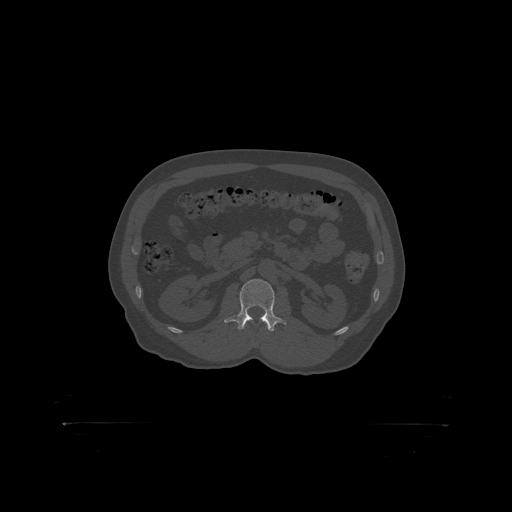
CT including the spine, one axial slice. Slice 302 of 399 in the series (ordered by position). Reconstruction kernel STANDARD. 120 kVp. Bone window (W 1800 / L 400 HU). 1.25 mm slice thickness. 512 × 512 image matrix. Male patient, age 46 years. From the clinical record (not read from this slice): primary cancer: skin.
Outlined on this slice (semi-automatic segmentation, software-assisted and operator-edited):
- L2 vertebra: bounding box [x1, y1, x2, y2] px = [238, 279, 275, 319]